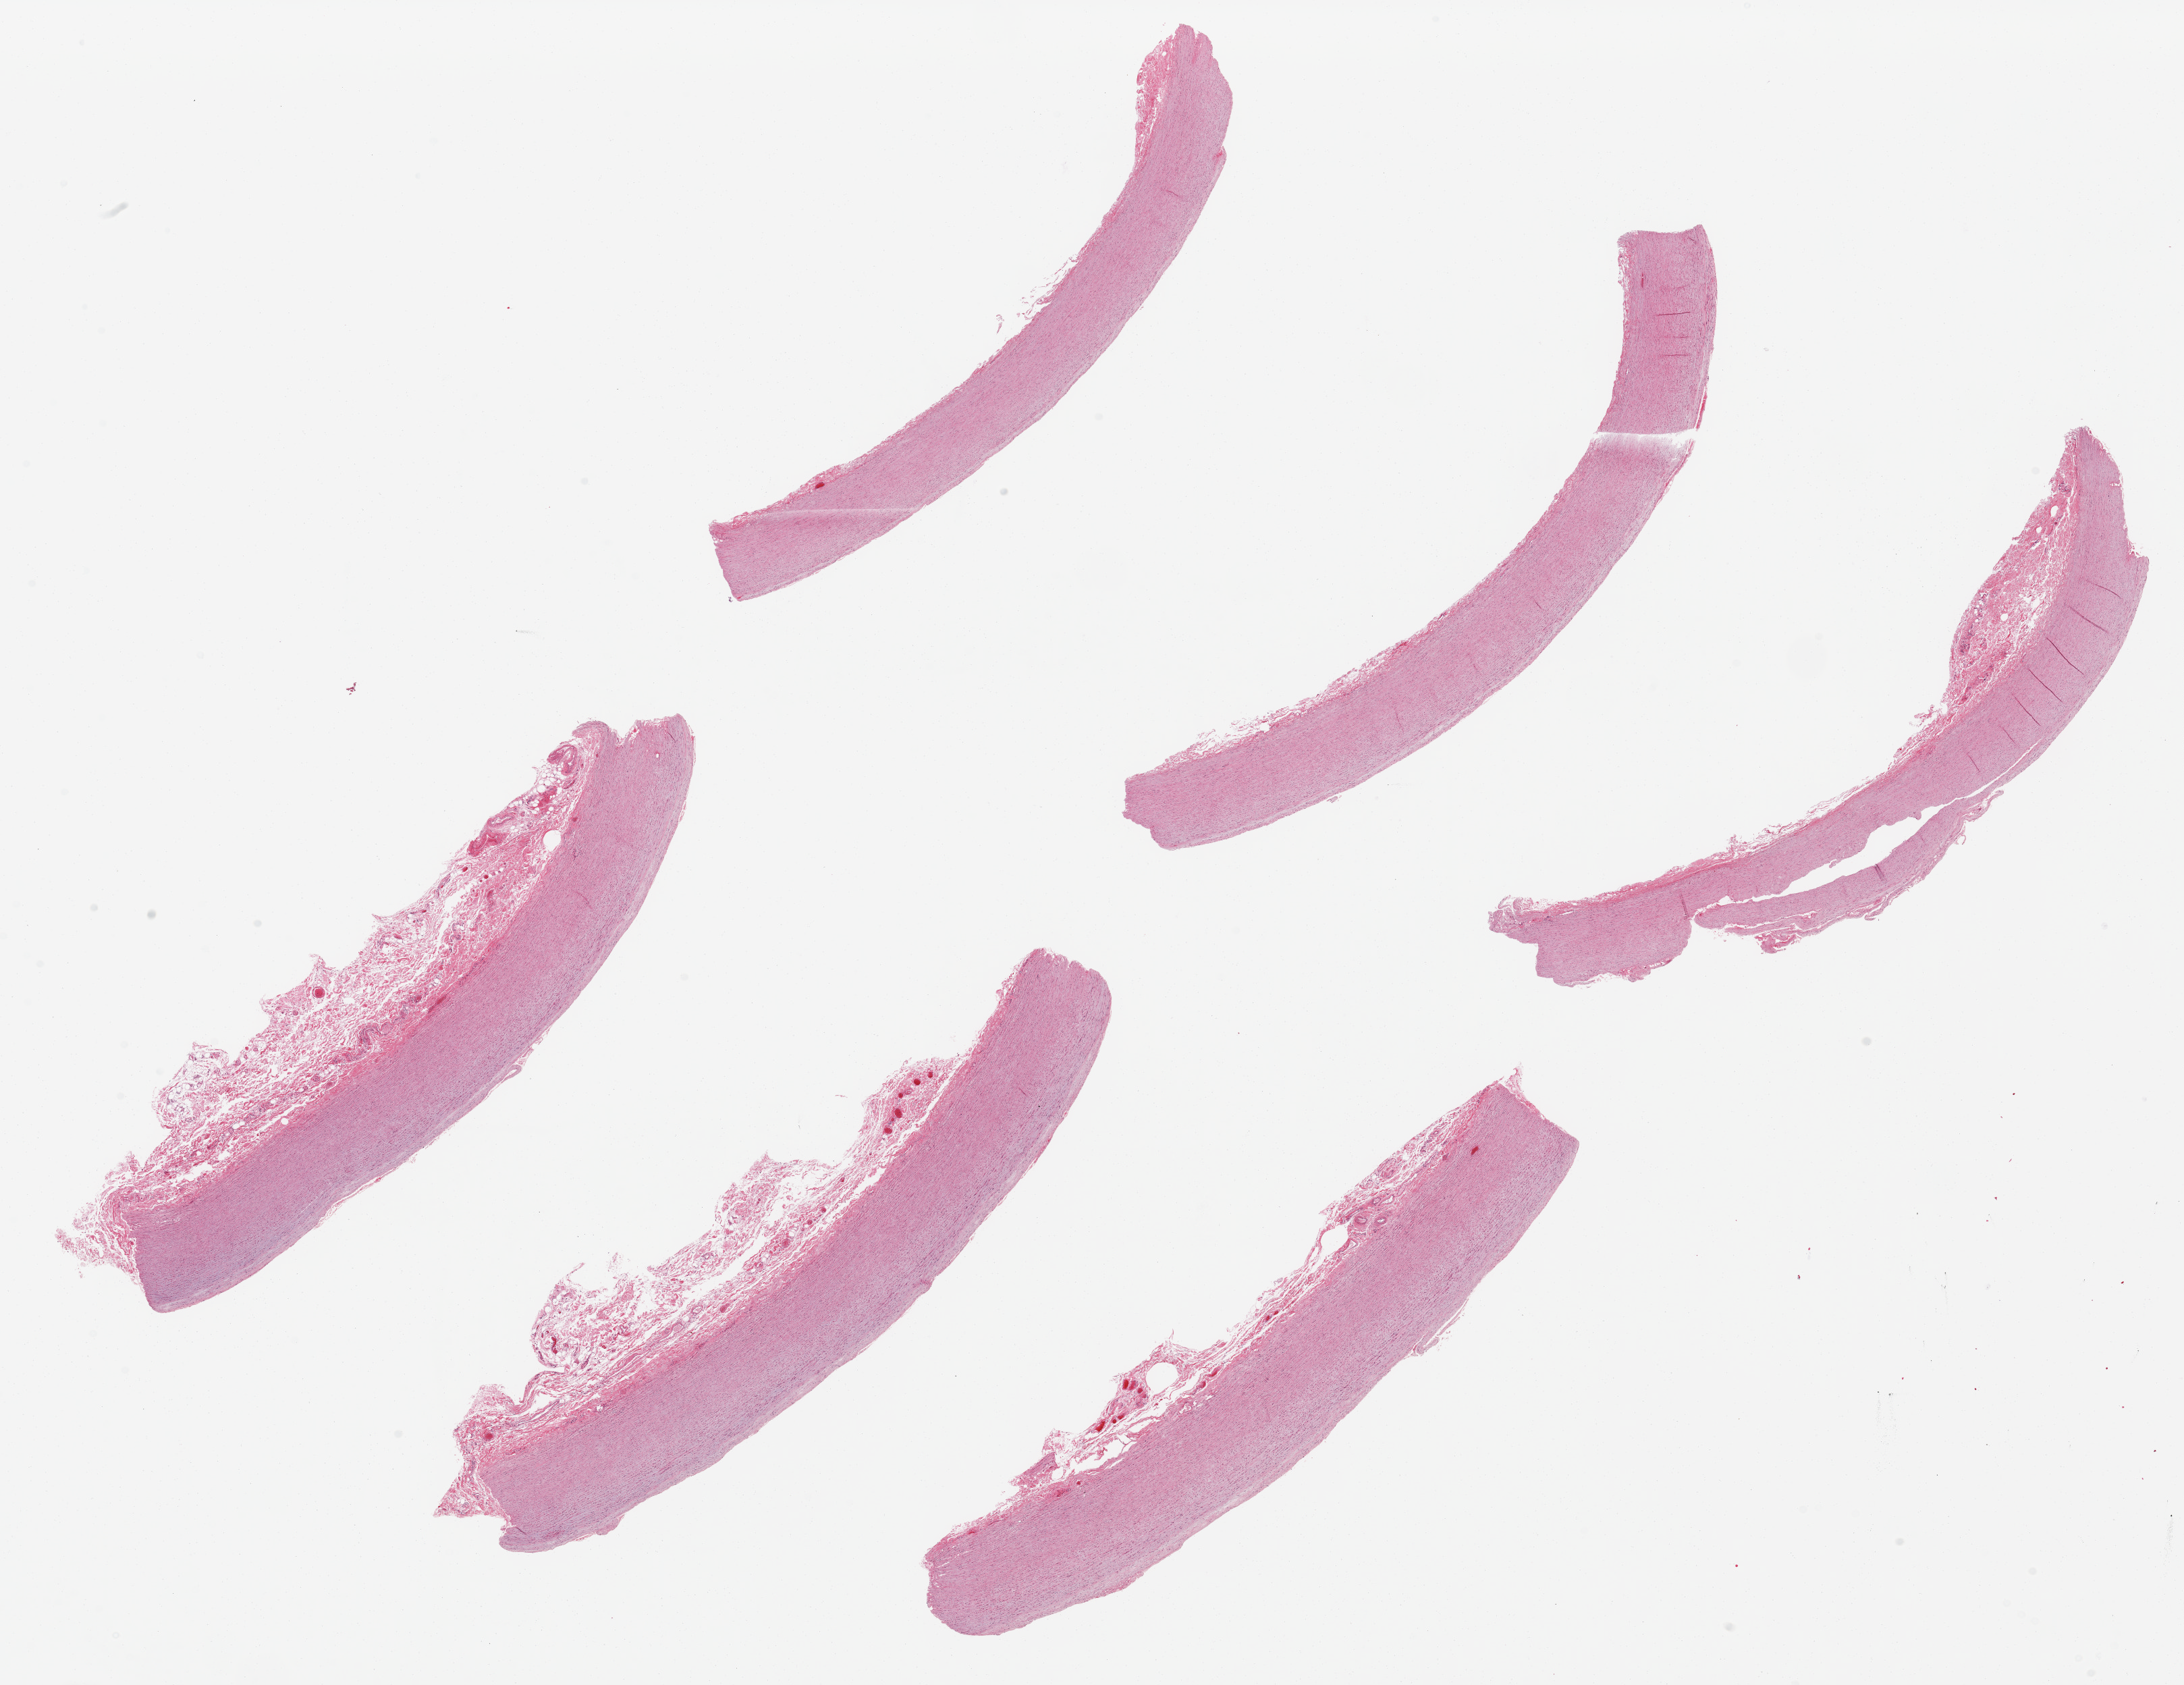
Digitized H&E-stained section, low-resolution overview of the scanned area, about 25.6 x 19.7 mm (acquisition: 20x scan), PAXgene-fixed, paraffin-embedded tissue, target tissue: aorta, donor tissue sample.
• pathologist's review note for this sample: 6 ~ 8.5x1mm 10.5x8.5 pieces